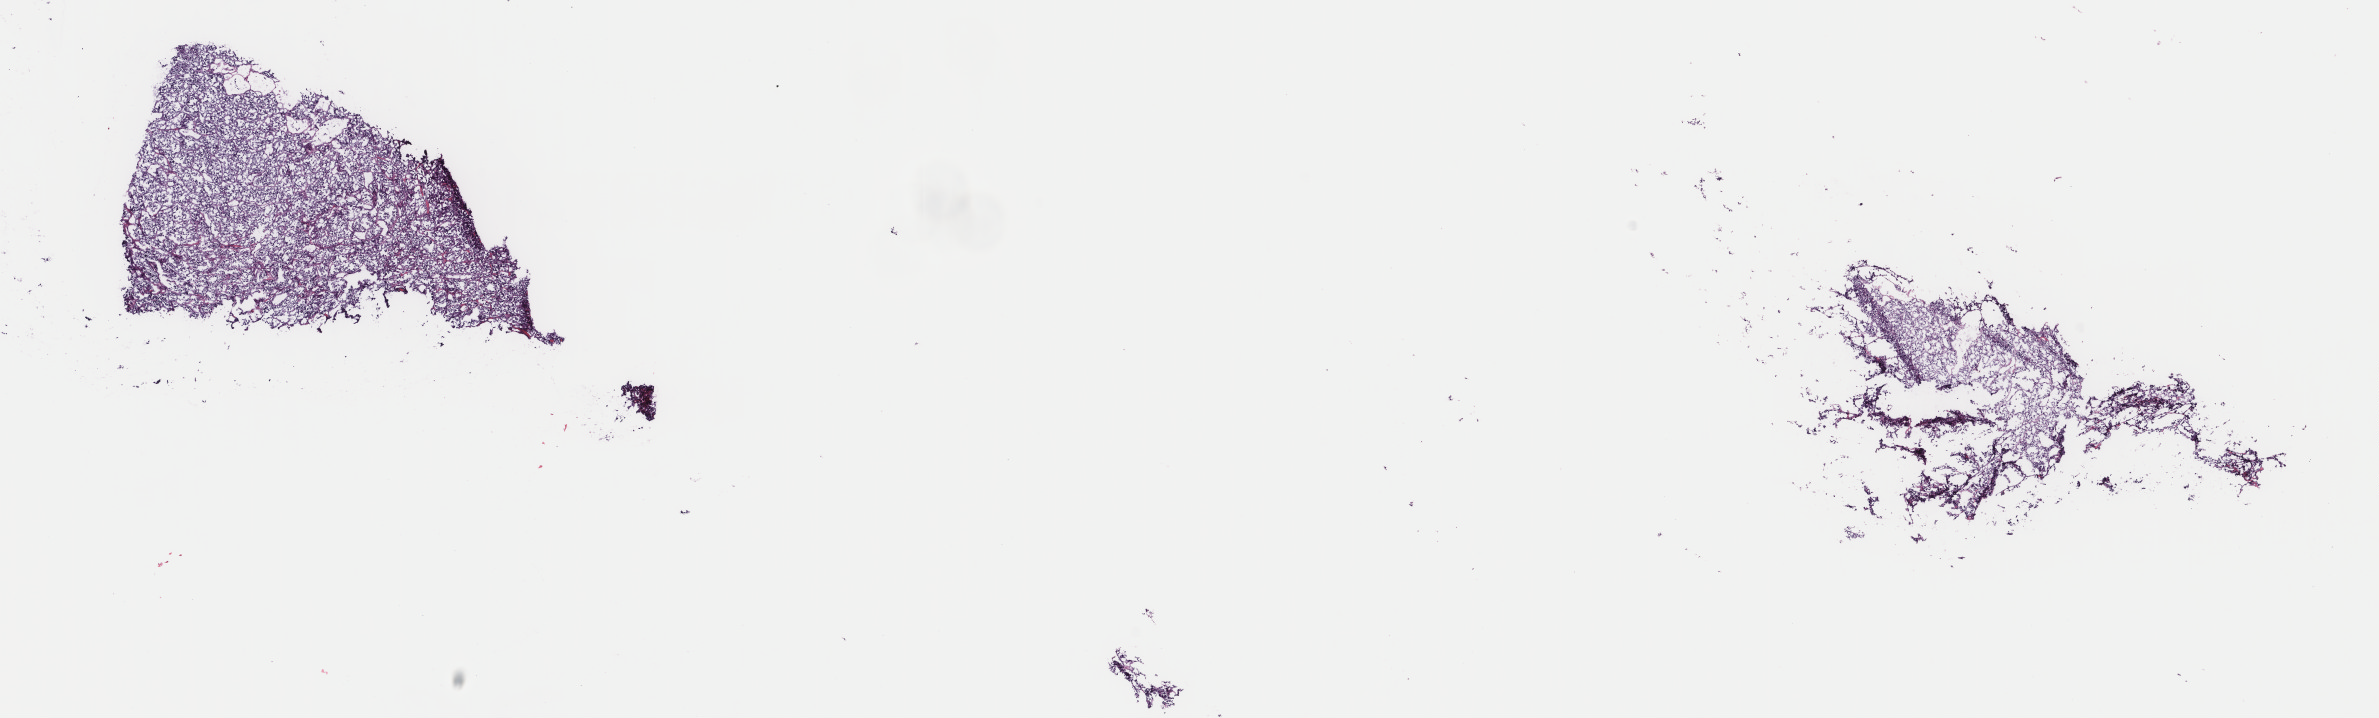
Whole-slide histology image, H&E — shown as a low-resolution overview of the whole scanned area (about 18.9 x 5.7 mm). Frozen section from the top of the tissue portion. Adrenal gland, additional new primary tumour sample. Male, age 31 years at initial diagnosis. Pathologist review of this section (percent, as recorded): tumour cells 95%, tumour nuclei 95%, normal cells 0%, stromal cells 5%, necrosis 0%. Infiltration values recorded for this section: lymphocyte infiltration 0%, monocyte infiltration 0%, neutrophil infiltration 0%.
This section: additional new primary tumour. Patient diagnosis: Pheochromocytoma, NOS.